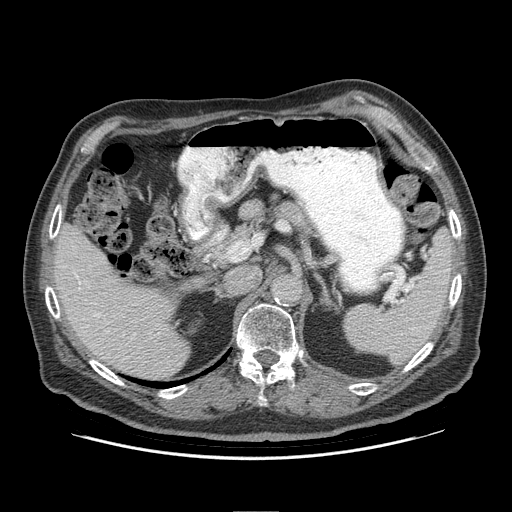
Contrast-enhanced abdominal CT (liver protocol), one axial slice. Slice 55 of 95 in the series (ordered by position). Reconstruction kernel STANDARD. 140 kVp. Soft-tissue window (W 400 / L 40 HU). 512 × 512 image matrix. Case-level facts recorded for this patient, not image findings: diagnosis: hepatocellular carcinoma (patient treated with transarterial chemoembolisation; whether this scan precedes or follows treatment is not stated here); TNM stage (as recorded): Stage-IVB; Child-Pugh class: A; tumour differentiation: well differentiated.
Outlined on this slice (semi-automatic segmentation, software-assisted and operator-edited):
- liver parenchyma outside the tumour (the mass and vessels are separate outlines, so this box may not span the whole liver): box from (x=54, y=224) to (x=190, y=378) px
- liver vessels: (x=75, y=274)–(x=97, y=316)